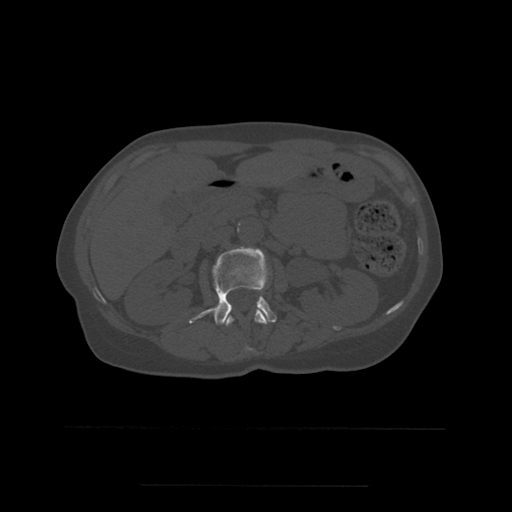
CT including the spine, one axial slice; position 220 of 544 along the scan axis; bone window (W 1800 / L 400 HU); 1.25 mm slice thickness; 512 × 512 image matrix, field of view 350 × 350 mm. Patient age 58 years. Case-level facts recorded for this patient, not image findings: primary cancer: lung.
Outlined on this slice (semi-automatic segmentation, software-assisted and operator-edited):
- L1 vertebra: bounding box (x1, y1, x2, y2) in pixels: (226, 310, 268, 351)
- L2 vertebra: (189, 247, 277, 325)